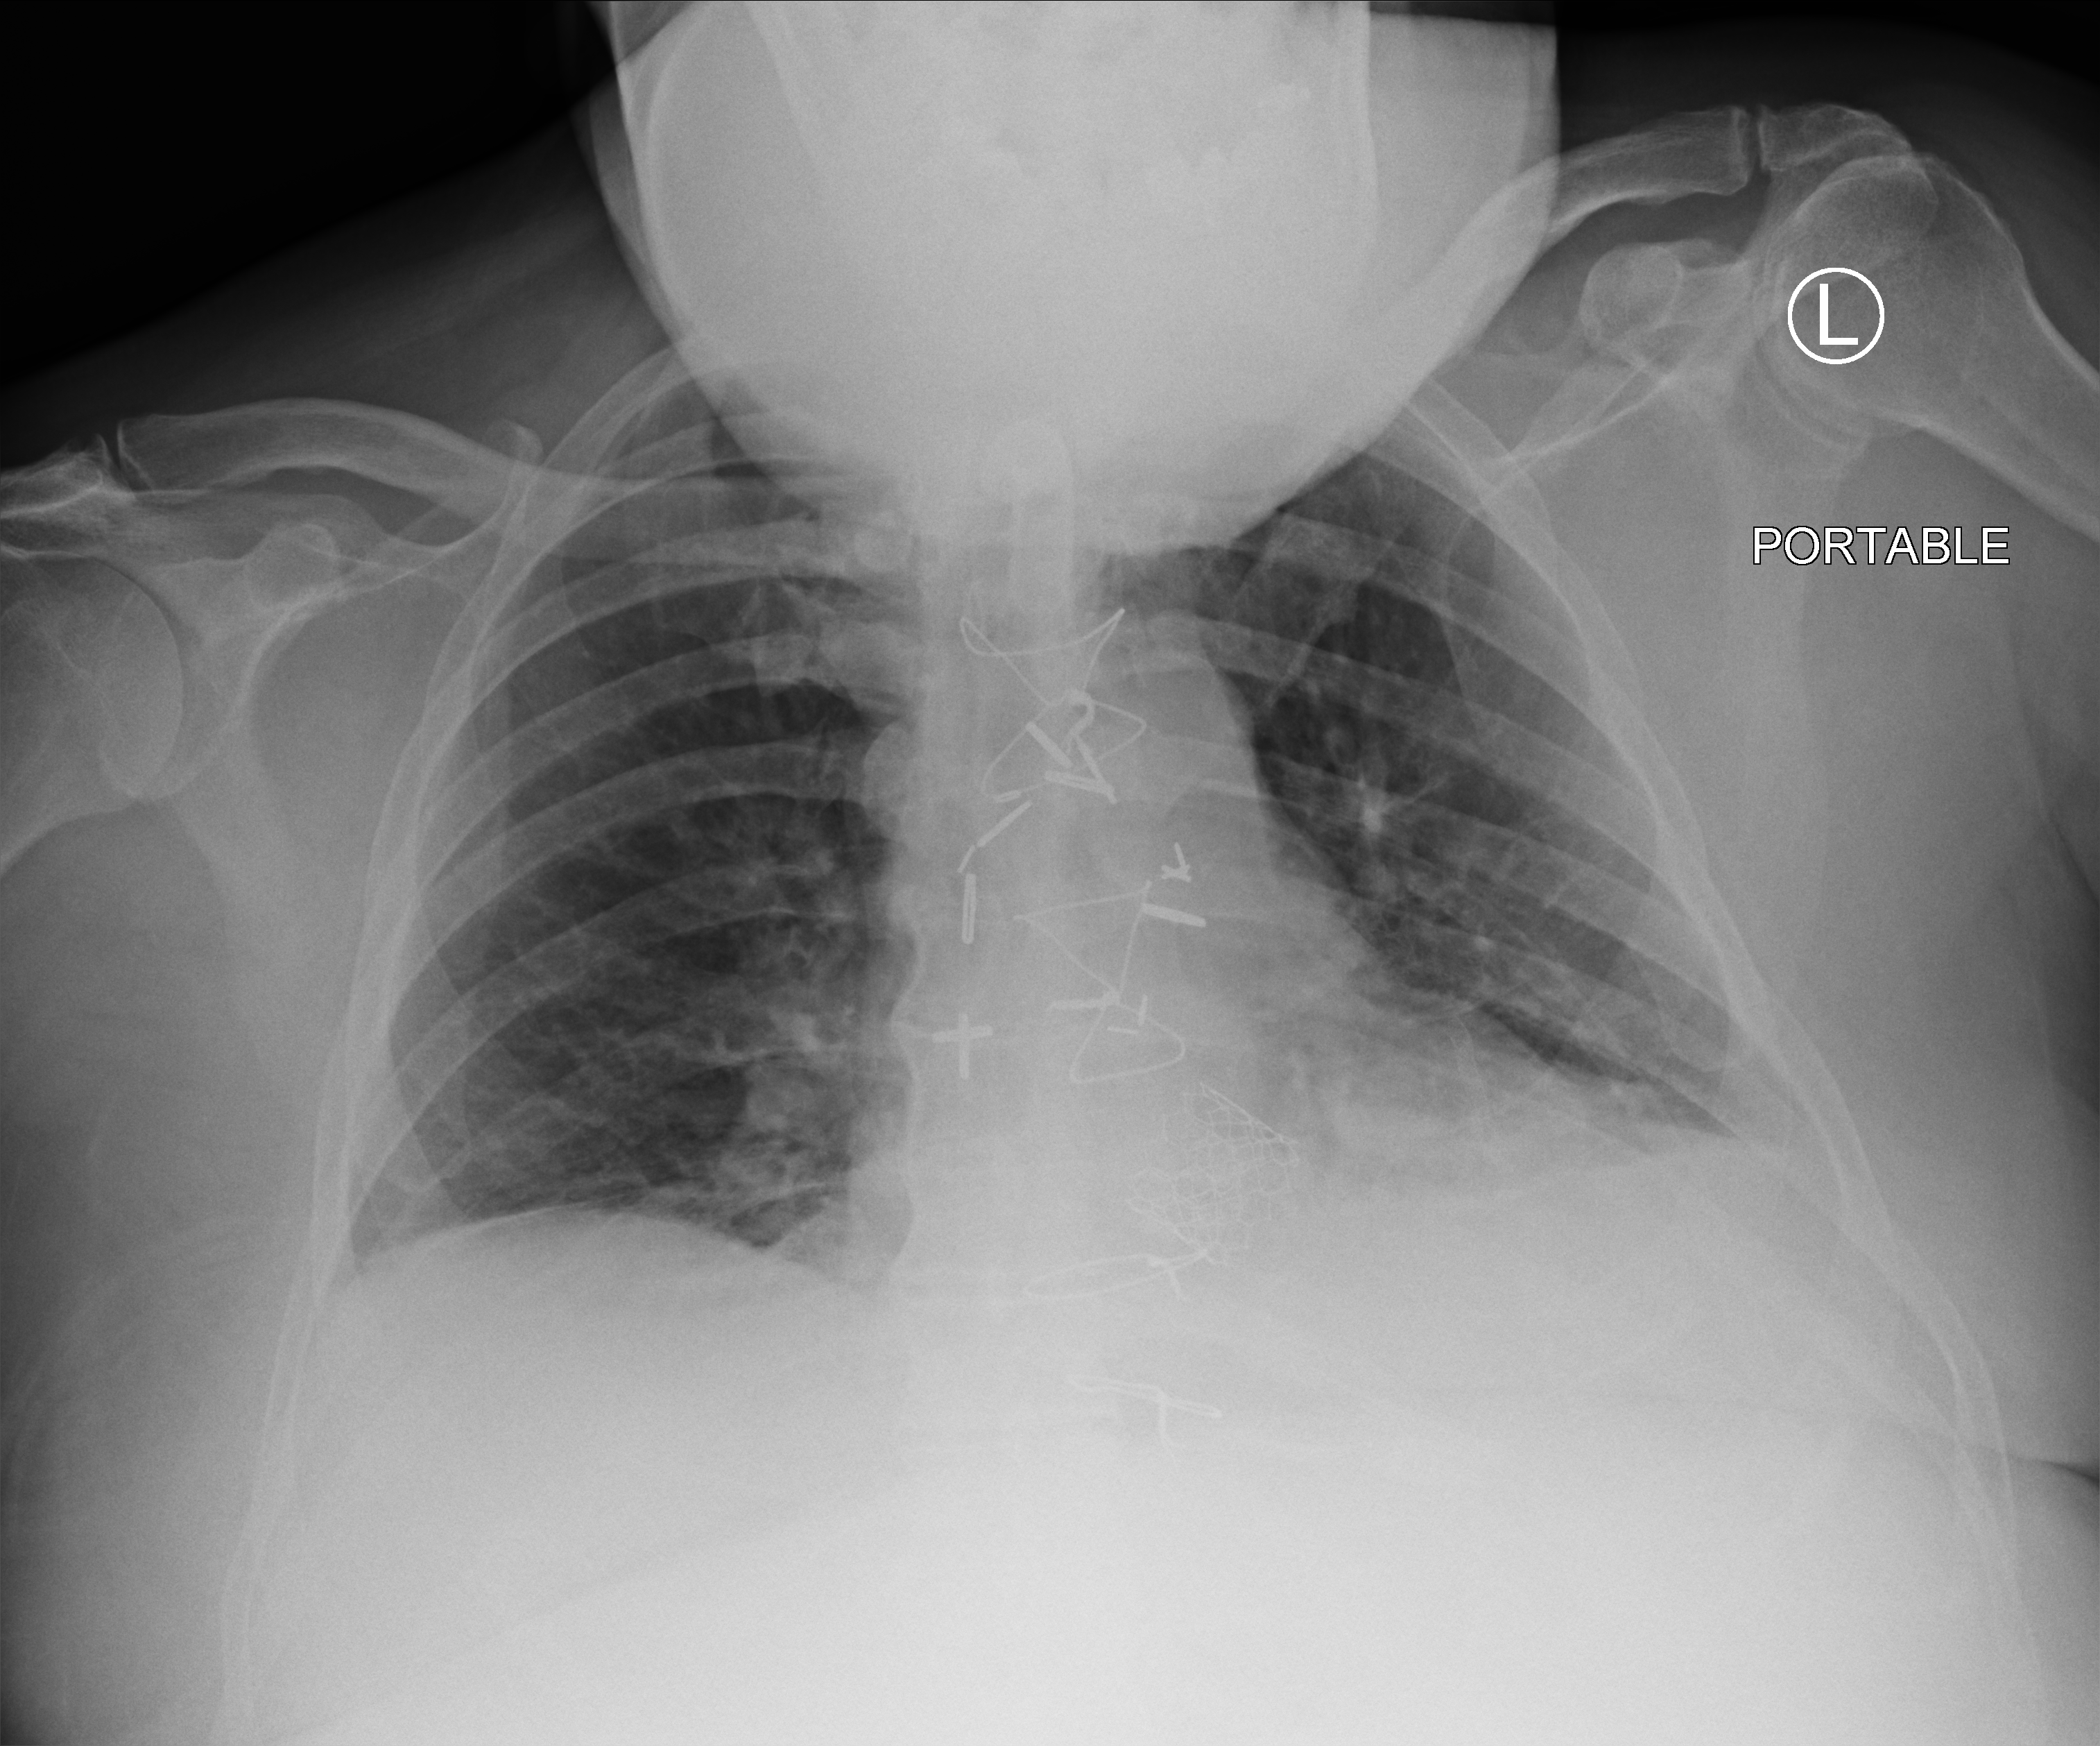
Portable chest radiograph; anteroposterior (AP) projection. Male patient hospitalised with COVID-19, age 60–74 years.
From the hospital-stay record, not from the radiograph (when in the stay this image was taken is not recorded):
- admitted to intensive care during this hospital stay: no
- COPD (admission record): no
- mechanically ventilated during this hospital stay: yes